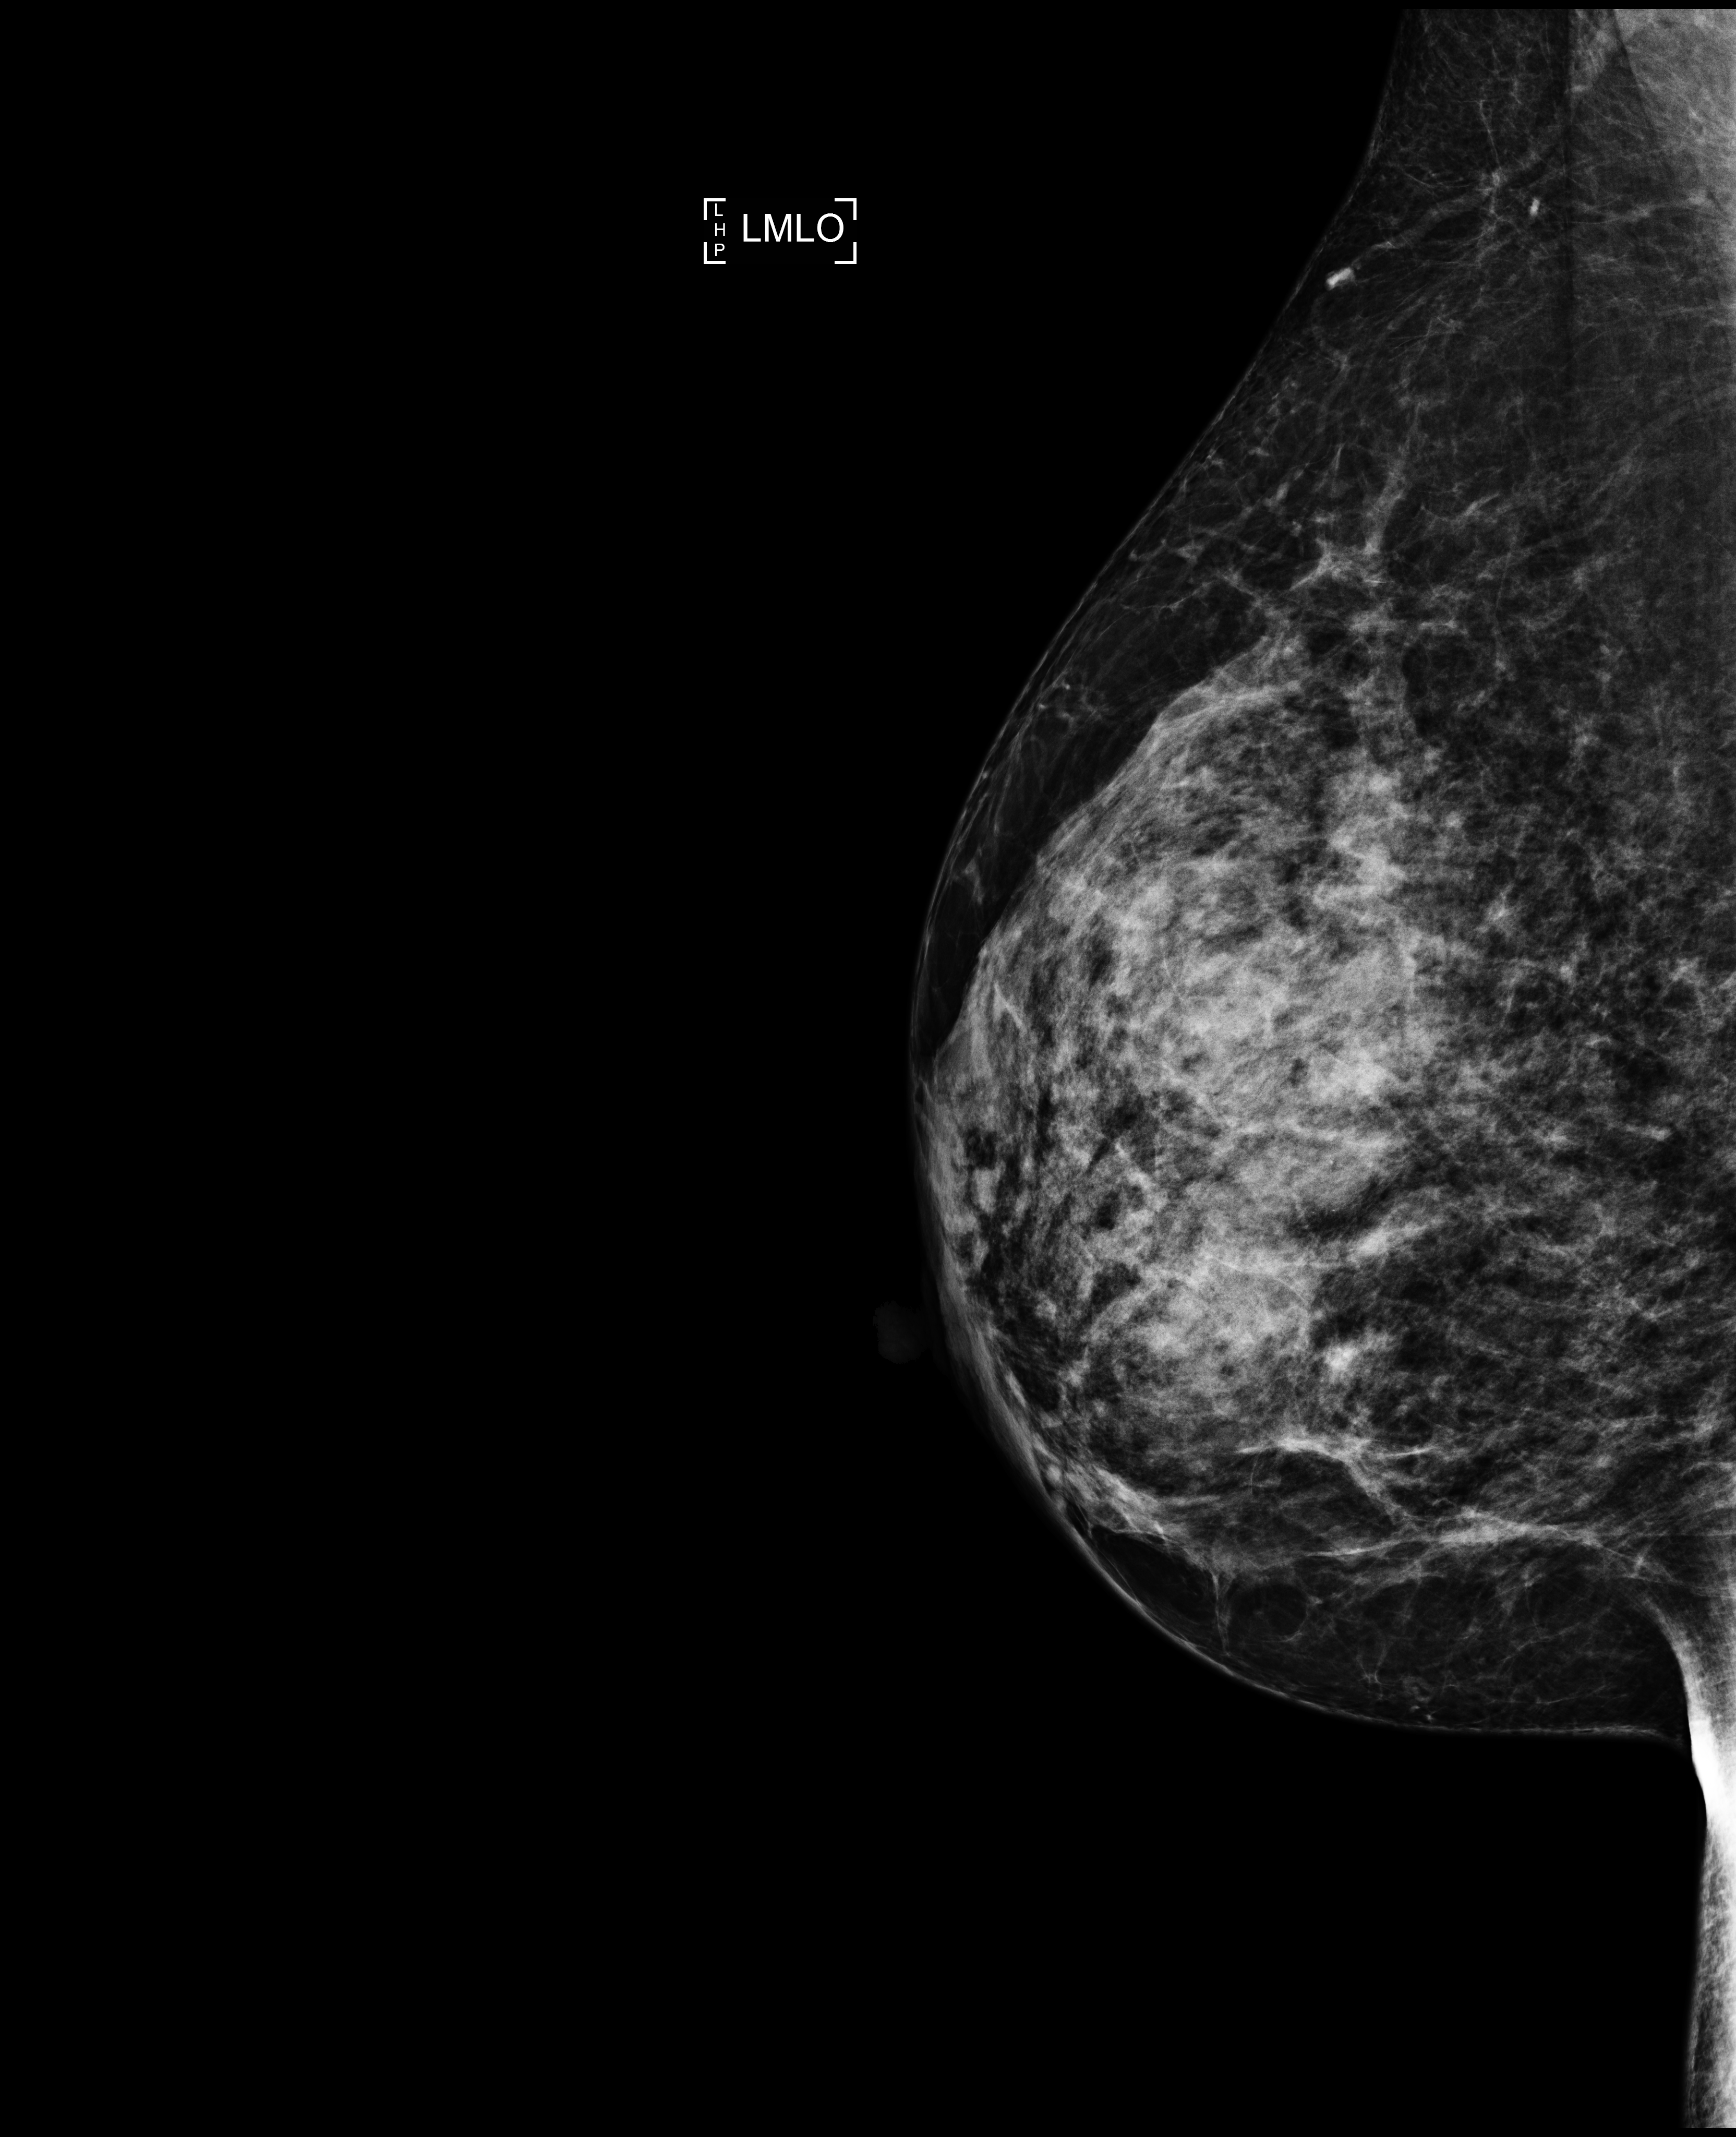
Full-field digital mammogram (FFDM), left breast, mediolateral oblique (MLO) view, annual screening mammography examination, system: Selenia Dimensions. Patient aged 42 years (female).
Final BI-RADS assessment for this screening round (tomosynthesis exam, both breasts): category 1.